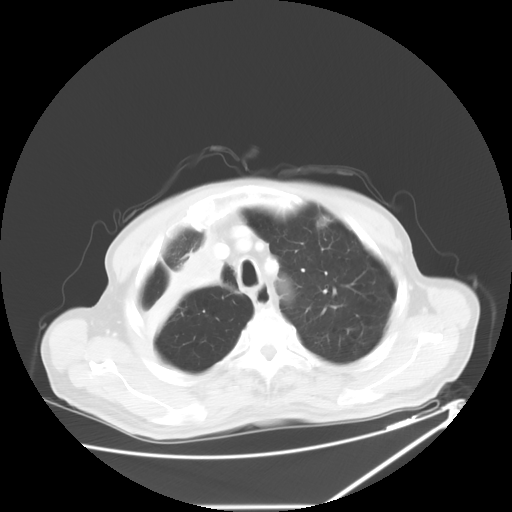
Chest CT, one axial slice; position 50 of 60 along the scan axis; 120 kVp; lung window (W 1500 / L -600 HU); 5 mm slice thickness; 512 × 512 image matrix. Patient: male, 73 years. Case-level facts recorded for this patient, not image findings: clinical TNM (as recorded): T2a N1 M0.
Annotated regions visible in this slice (rectangle marked by the reading radiologist):
- lung tumour (recorded histology: squamous cell carcinoma): bounding box <140,232,228,345> (left, top, right, bottom; pixels)